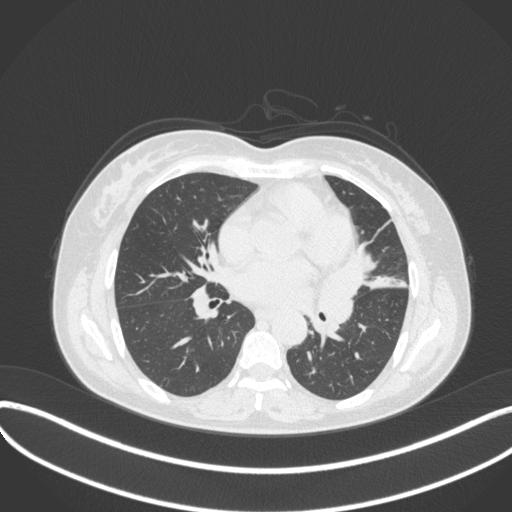
Chest CT, one axial slice; position 172 of 373 along the scan axis; reconstruction kernel B31f; 120 kVp; lung window (W 1500 / L -600 HU); 512 × 512 image matrix, field of view 400 × 400 mm. Patient: female, 54 years. From the clinical record (not read from this slice): clinical TNM (as recorded): T2a N1 M0; histopathological grade: G3.
Outlined on this slice (rectangle marked by the reading radiologist):
- lung tumour (recorded histology: small cell carcinoma): bounding box (x1, y1, x2, y2) in pixels: (313, 242, 371, 342)